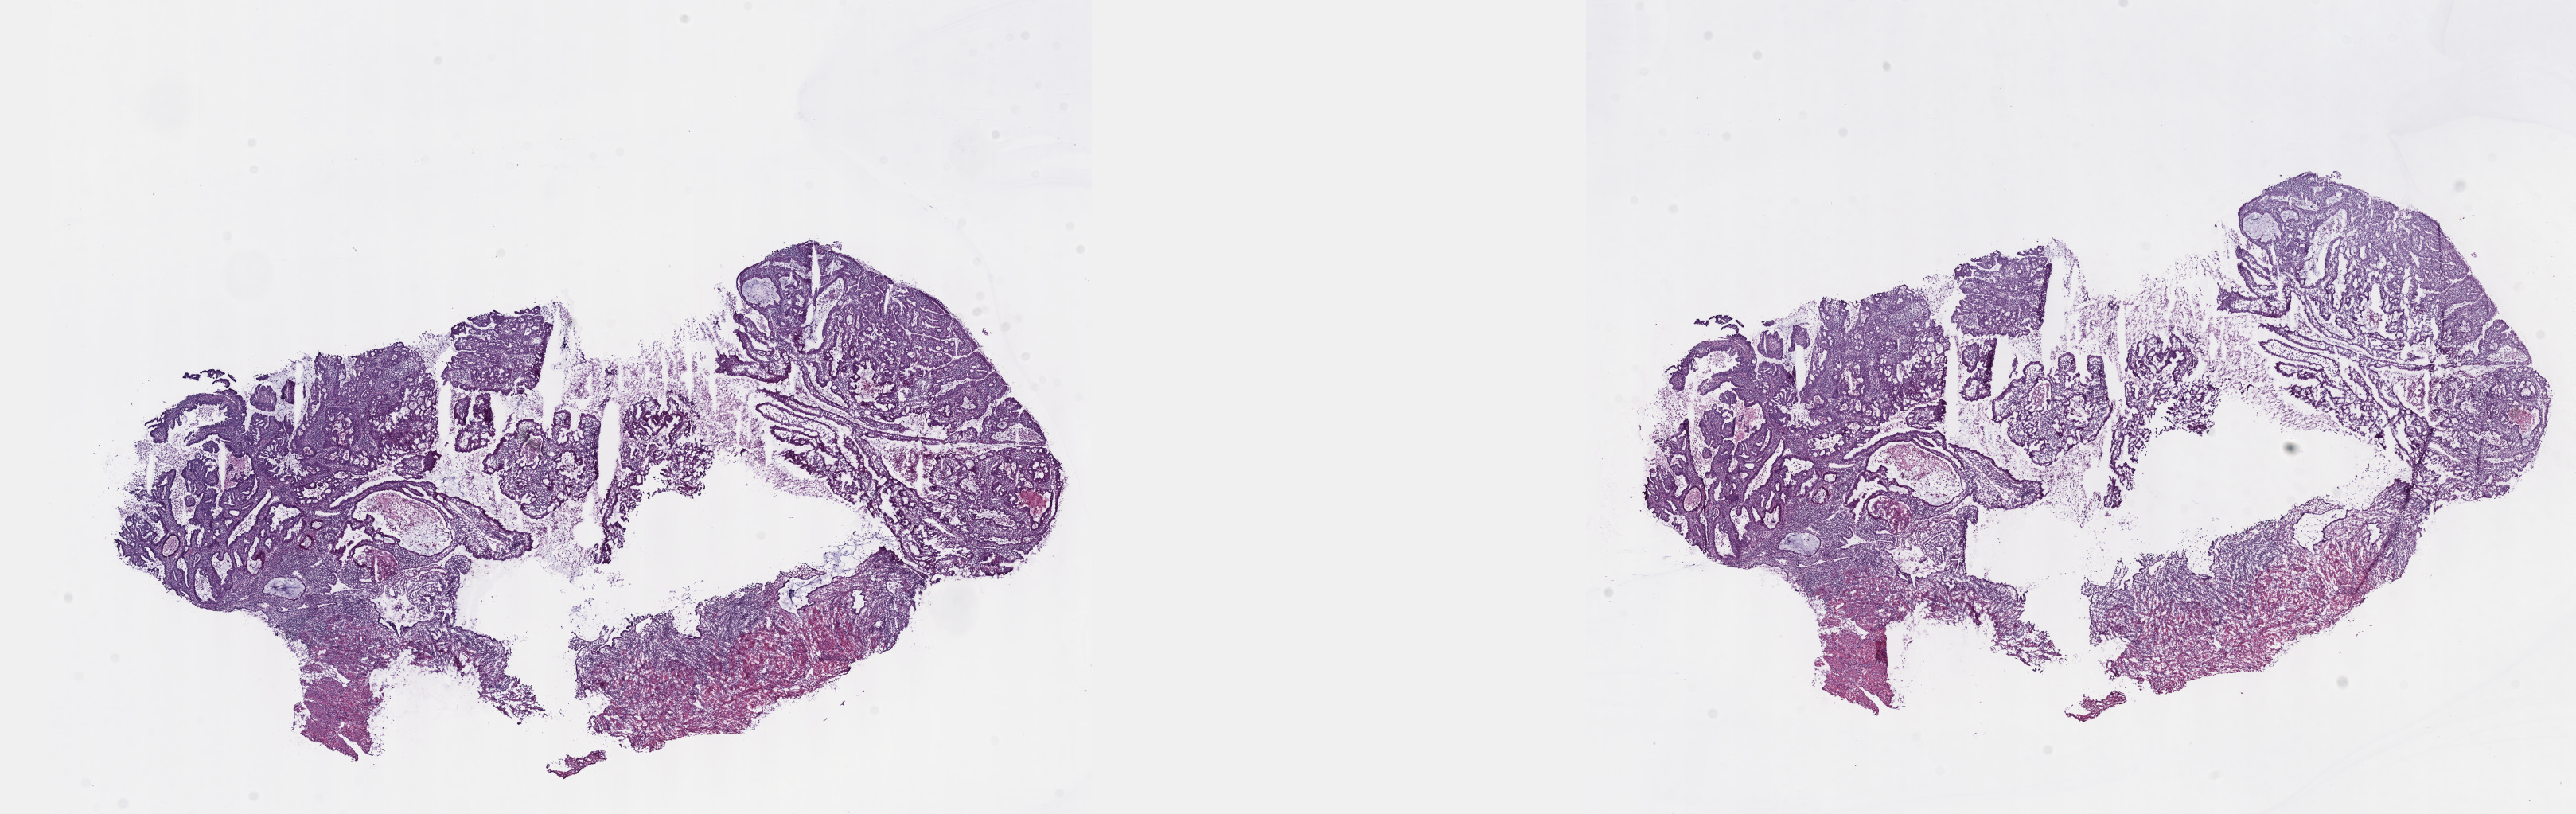
Digitized Hematoxylin and eosin (H&E) stained tissue section (whole slide), shown as a low-resolution overview of the whole scanned area (about 26.2 x 8.3 mm, slide scanned at 40x). Frozen section from the top of the tissue portion. Sample: primary tumour, cervix. Patient: female, age at initial diagnosis 61 years. Histologic grade: G2 (moderately differentiated). Slide review estimates, as recorded: tumour cells 85%, tumour nuclei 60%, normal cells 15%, stromal cells 0%, necrosis 0%. Infiltration values recorded for this section: lymphocyte infiltration 10%, monocyte infiltration 2%, neutrophil infiltration 3%.
* FIGO stage: IB1
* pathologic diagnosis: Mucinous adenocarcinoma, endocervical type (cervix uteri)